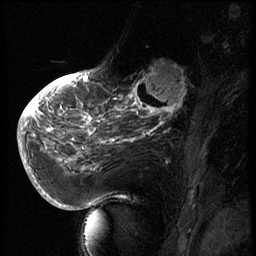
Breast MRI (dynamic contrast-enhanced), one sagittal slice; slice 24 of 66 in the series (ordered by position); 3 images stored at this slice position (order not interpretable as contrast timing); 1.5 T; TE 4.2 ms, TR 8.9 ms; 2.5 mm slice thickness; 256 × 256 image matrix. Patient: female, 56 years. From the clinical record (not read from this slice): setting: breast cancer imaged before/during neoadjuvant chemotherapy.
Outlined on this slice (semi-automatically segmented with operator editing):
- analysis volume of interest (the breast-tissue region the enhancement analysis was run in; not a lesion): box from (x=129, y=62) to (x=194, y=127) px
- tumour enhancement mask (voxels above the 140 % enhancement threshold inside the analysis volume of interest): (x=129, y=64)–(x=188, y=127)